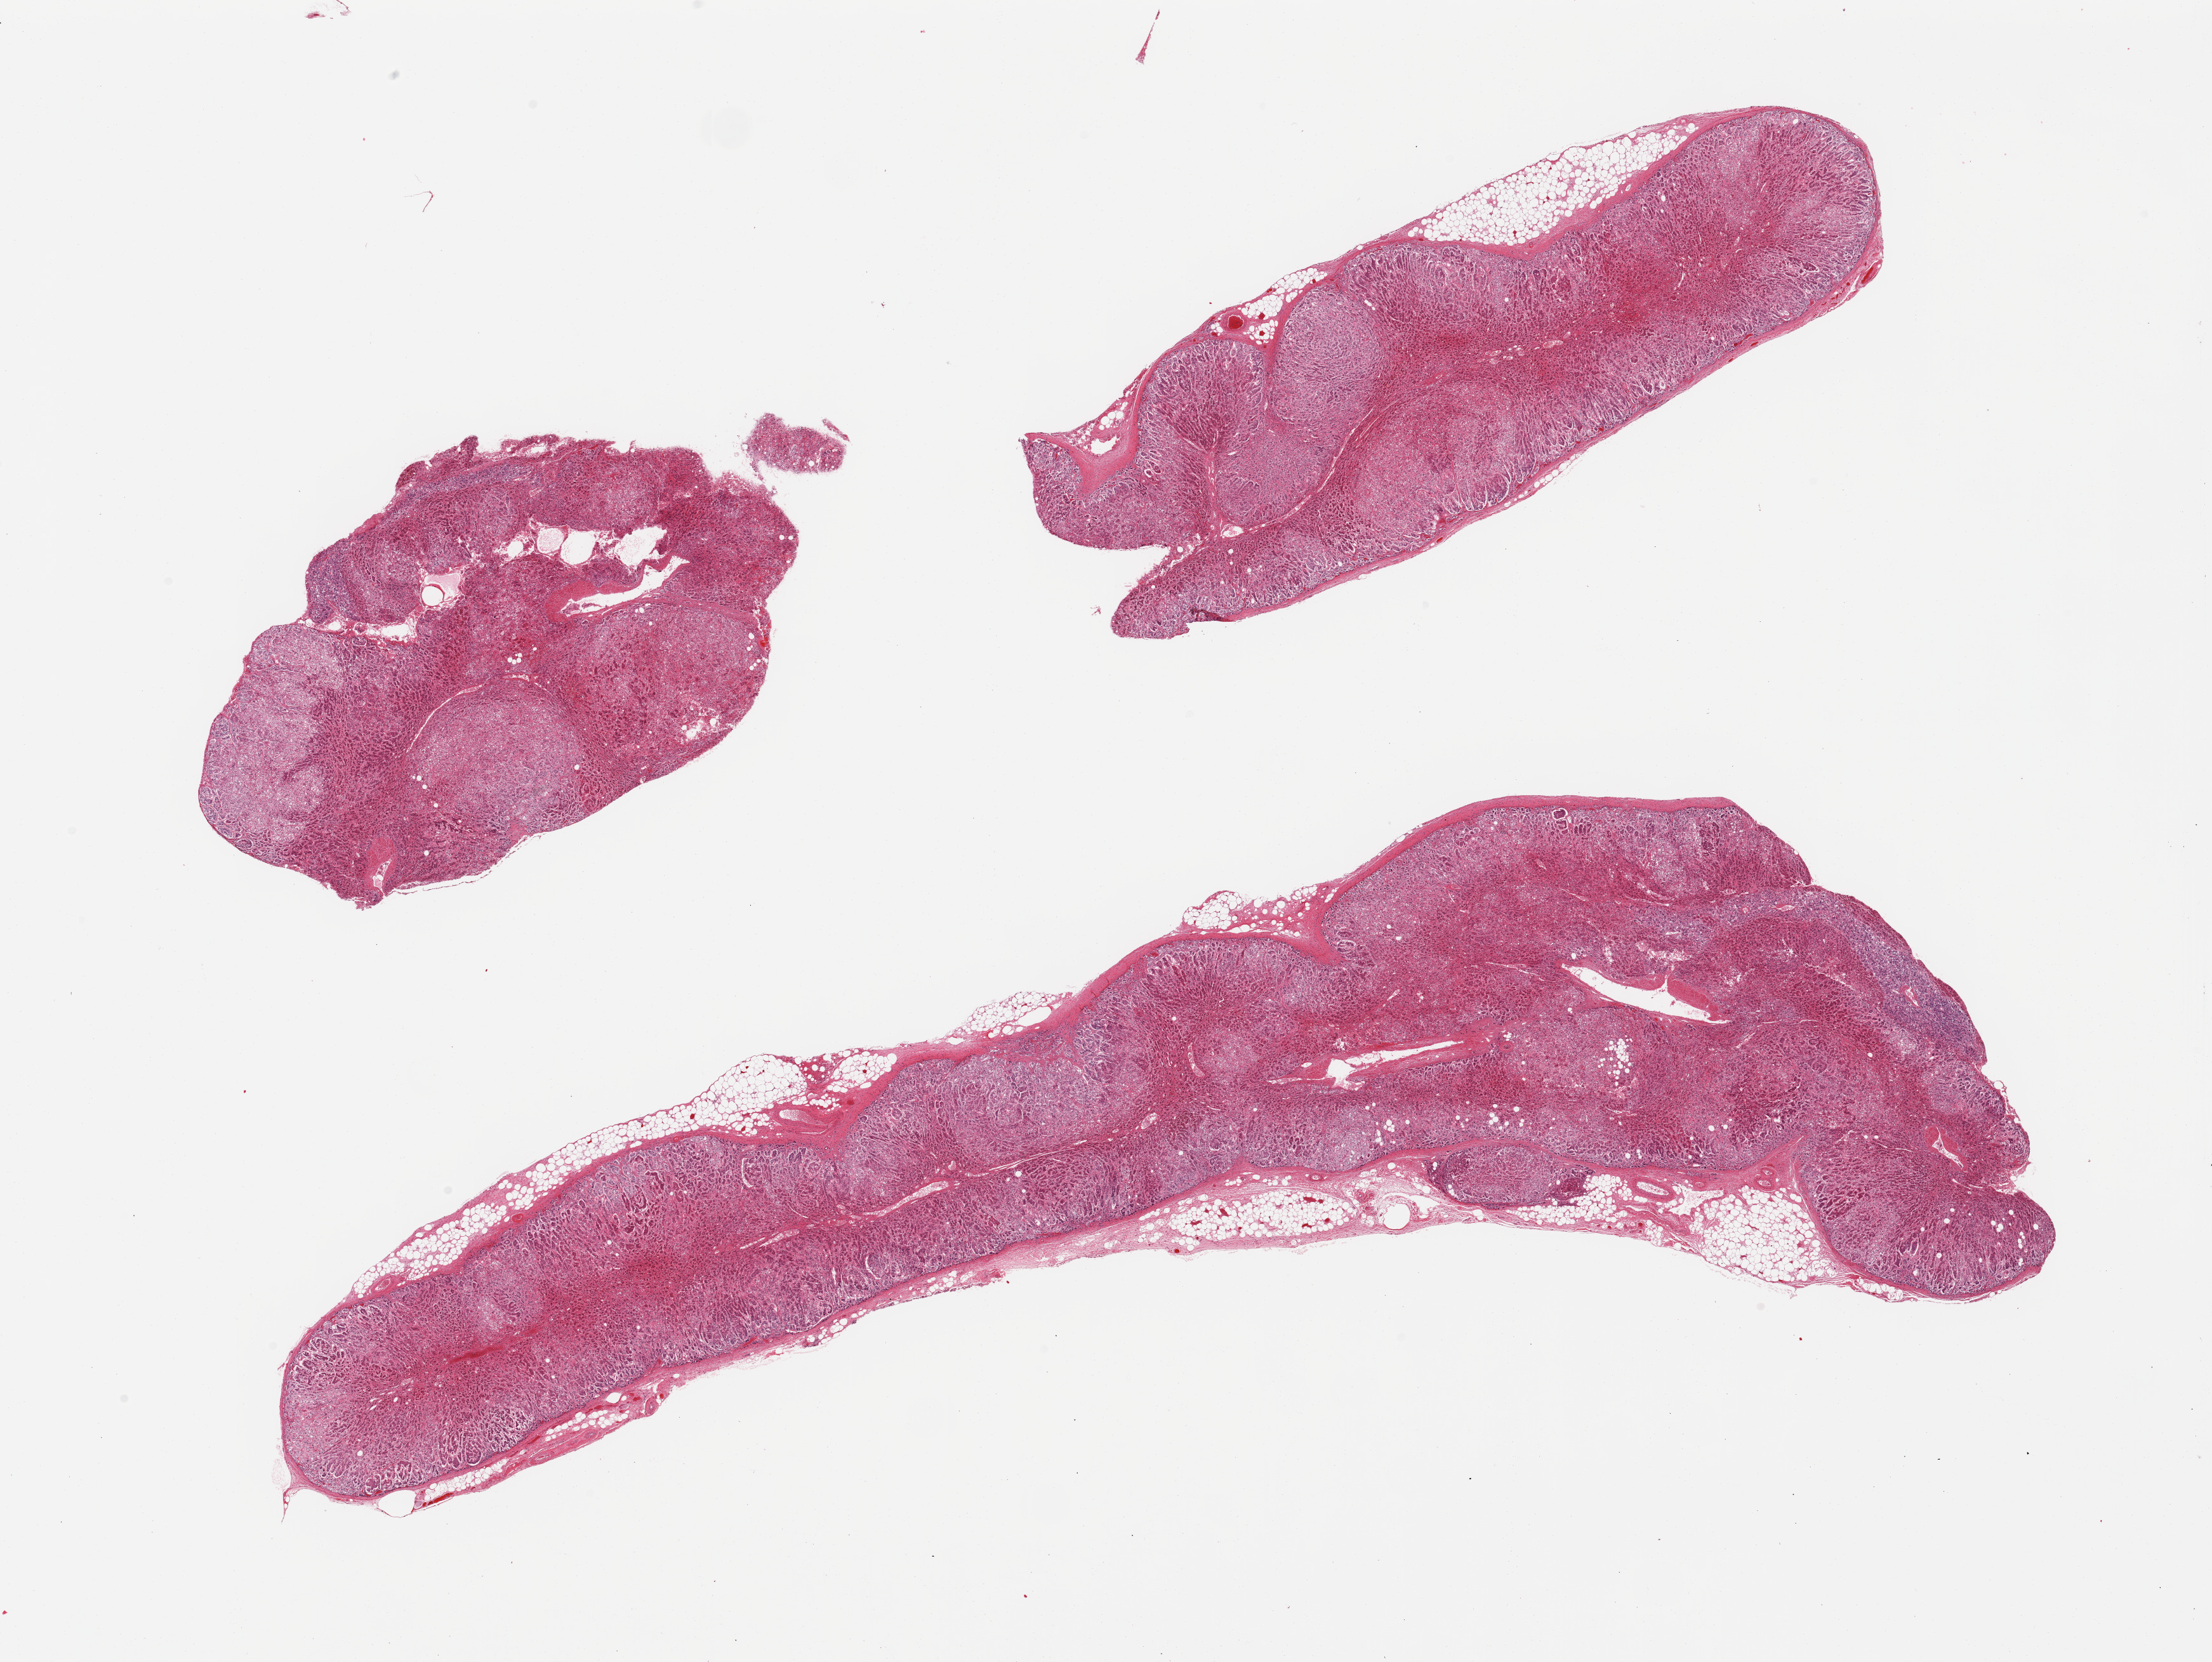
Digitized hematoxylin and eosin (H&E)-stained section, whole scanned area (about 27.6 x 20.7 mm, acquisition: 20x scan) shown as a low-resolution overview; PAXgene-fixed paraffin-embedded (PFPE) section; section of adrenal gland (target tissue); tissue donor sample. Male donor.
Pathologist's review note for this sample: 3 pieces; cortex and medulla ; less than 10% external fat.